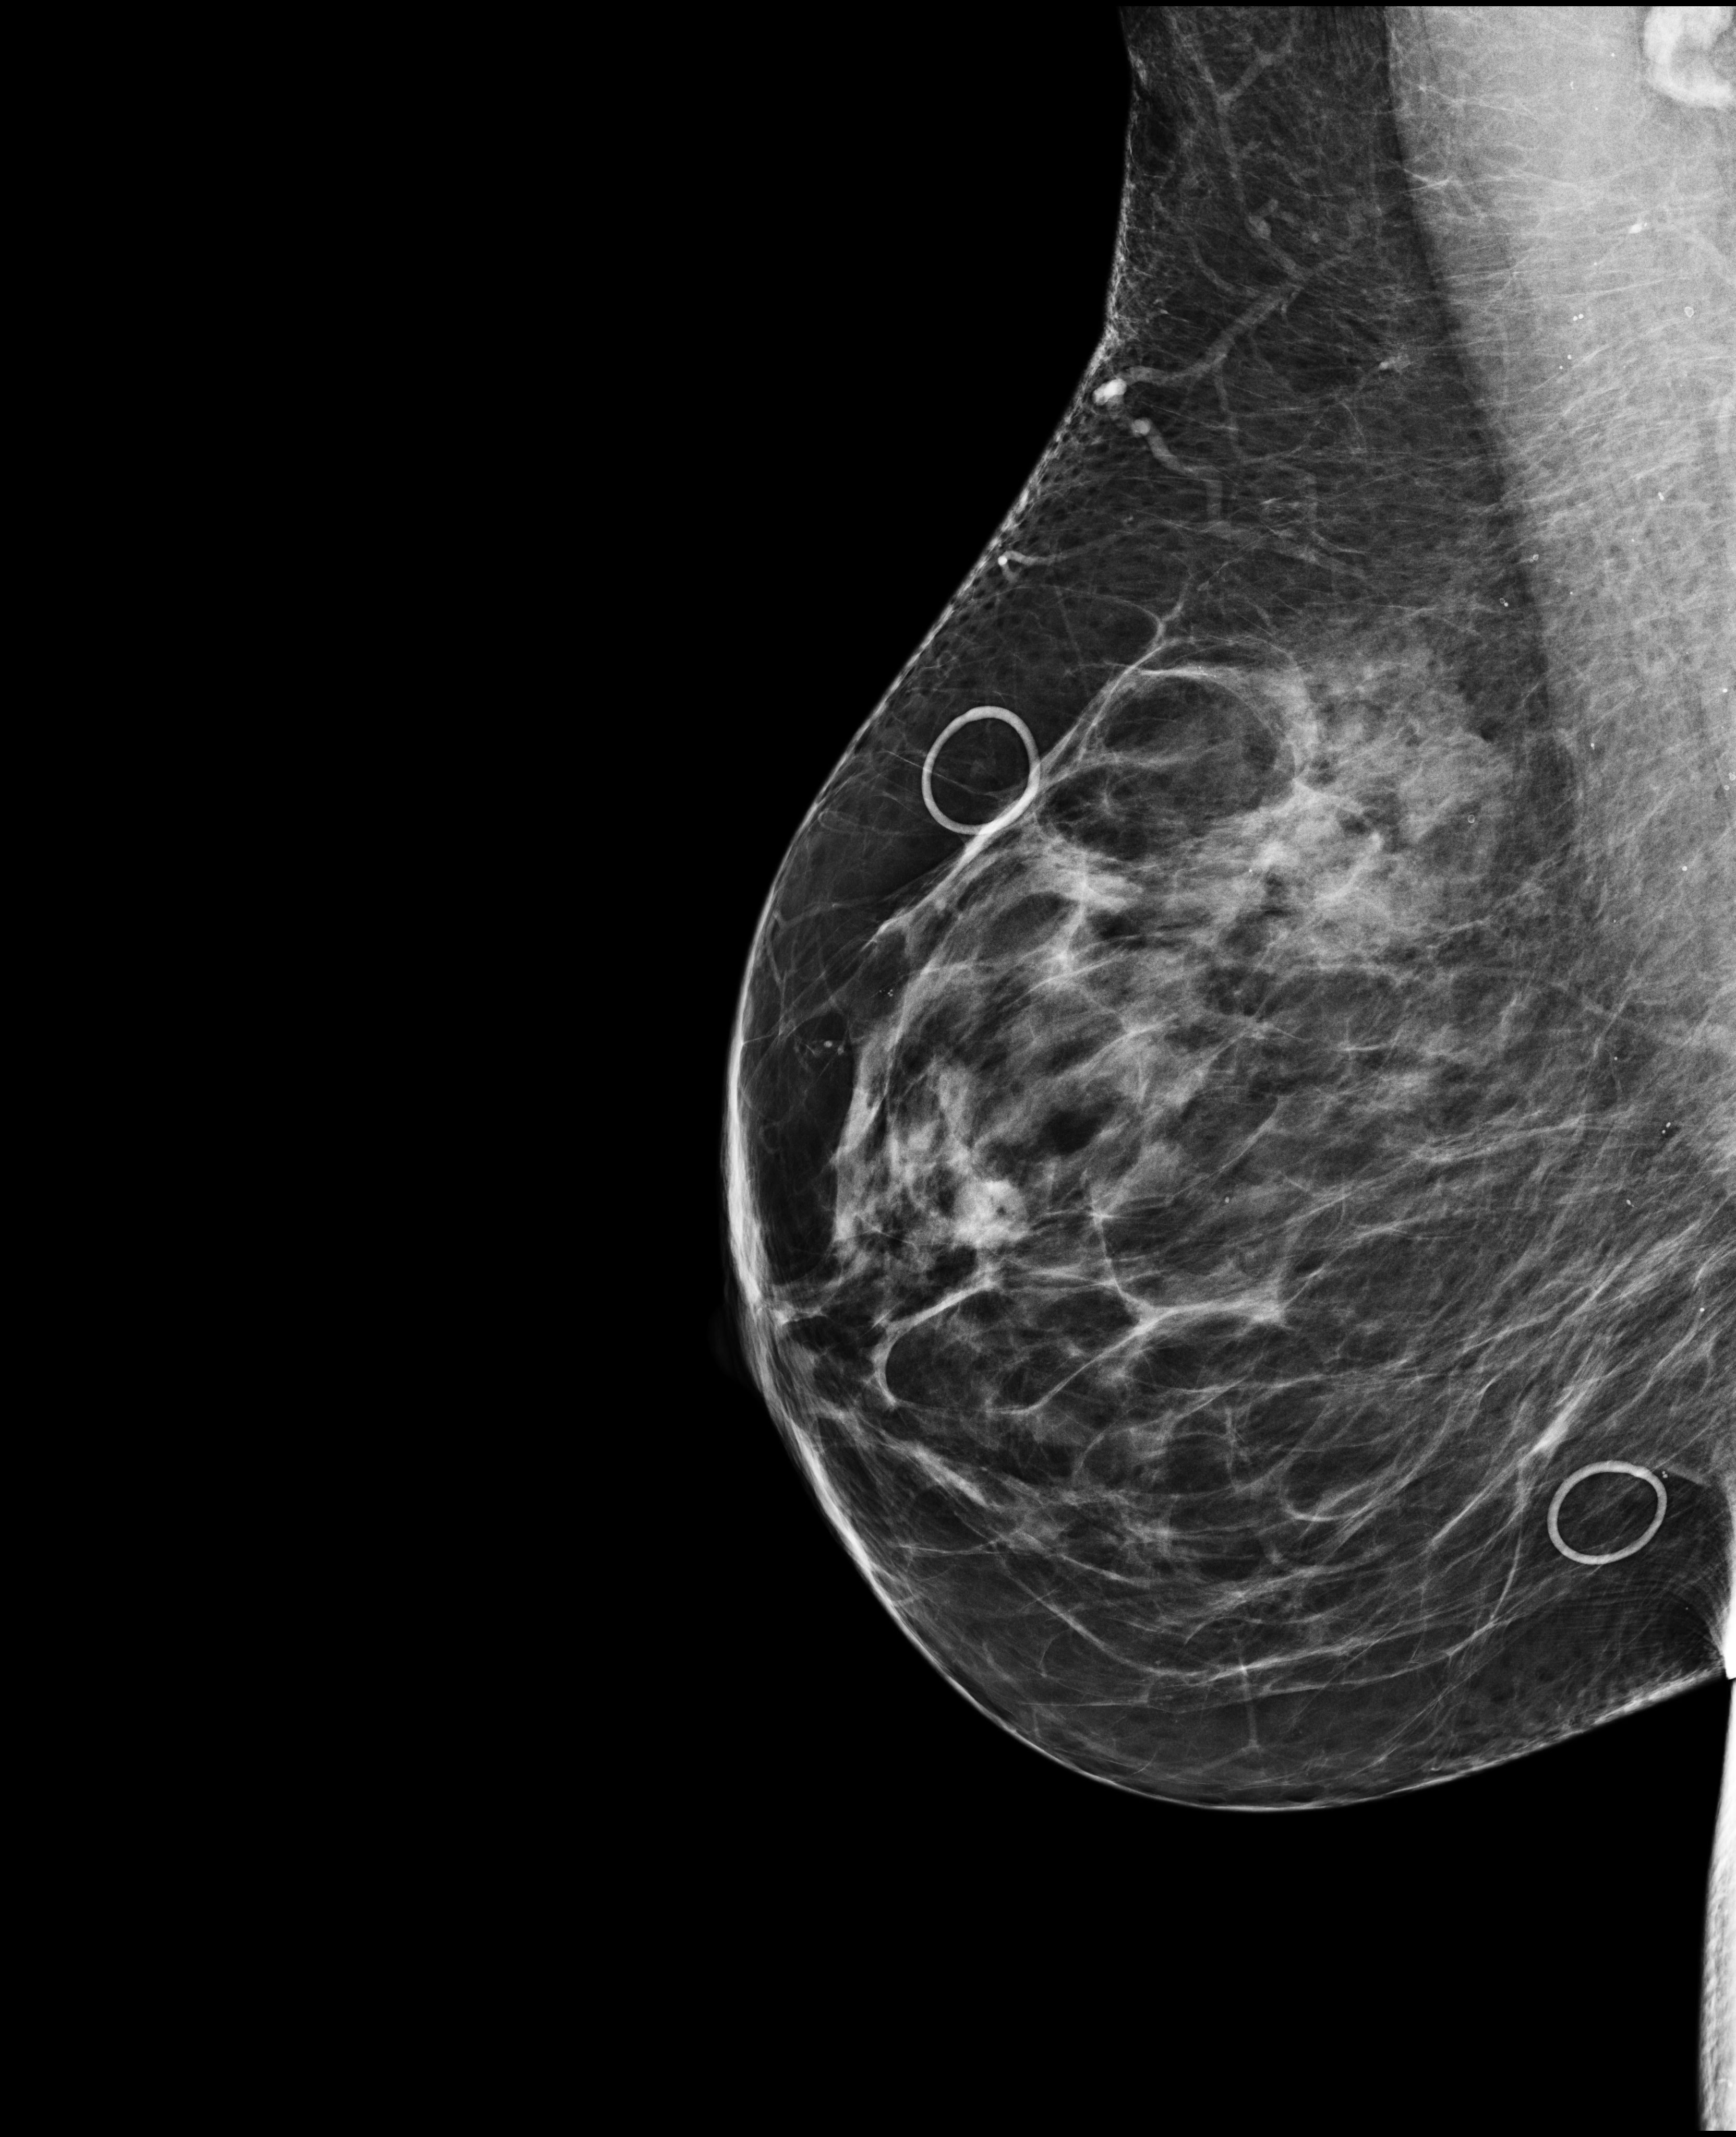
Screening examination. Female patient, age 60 years.
Image type: full-field digital mammogram. Breast: right. Projection: medio-lateral oblique projection.